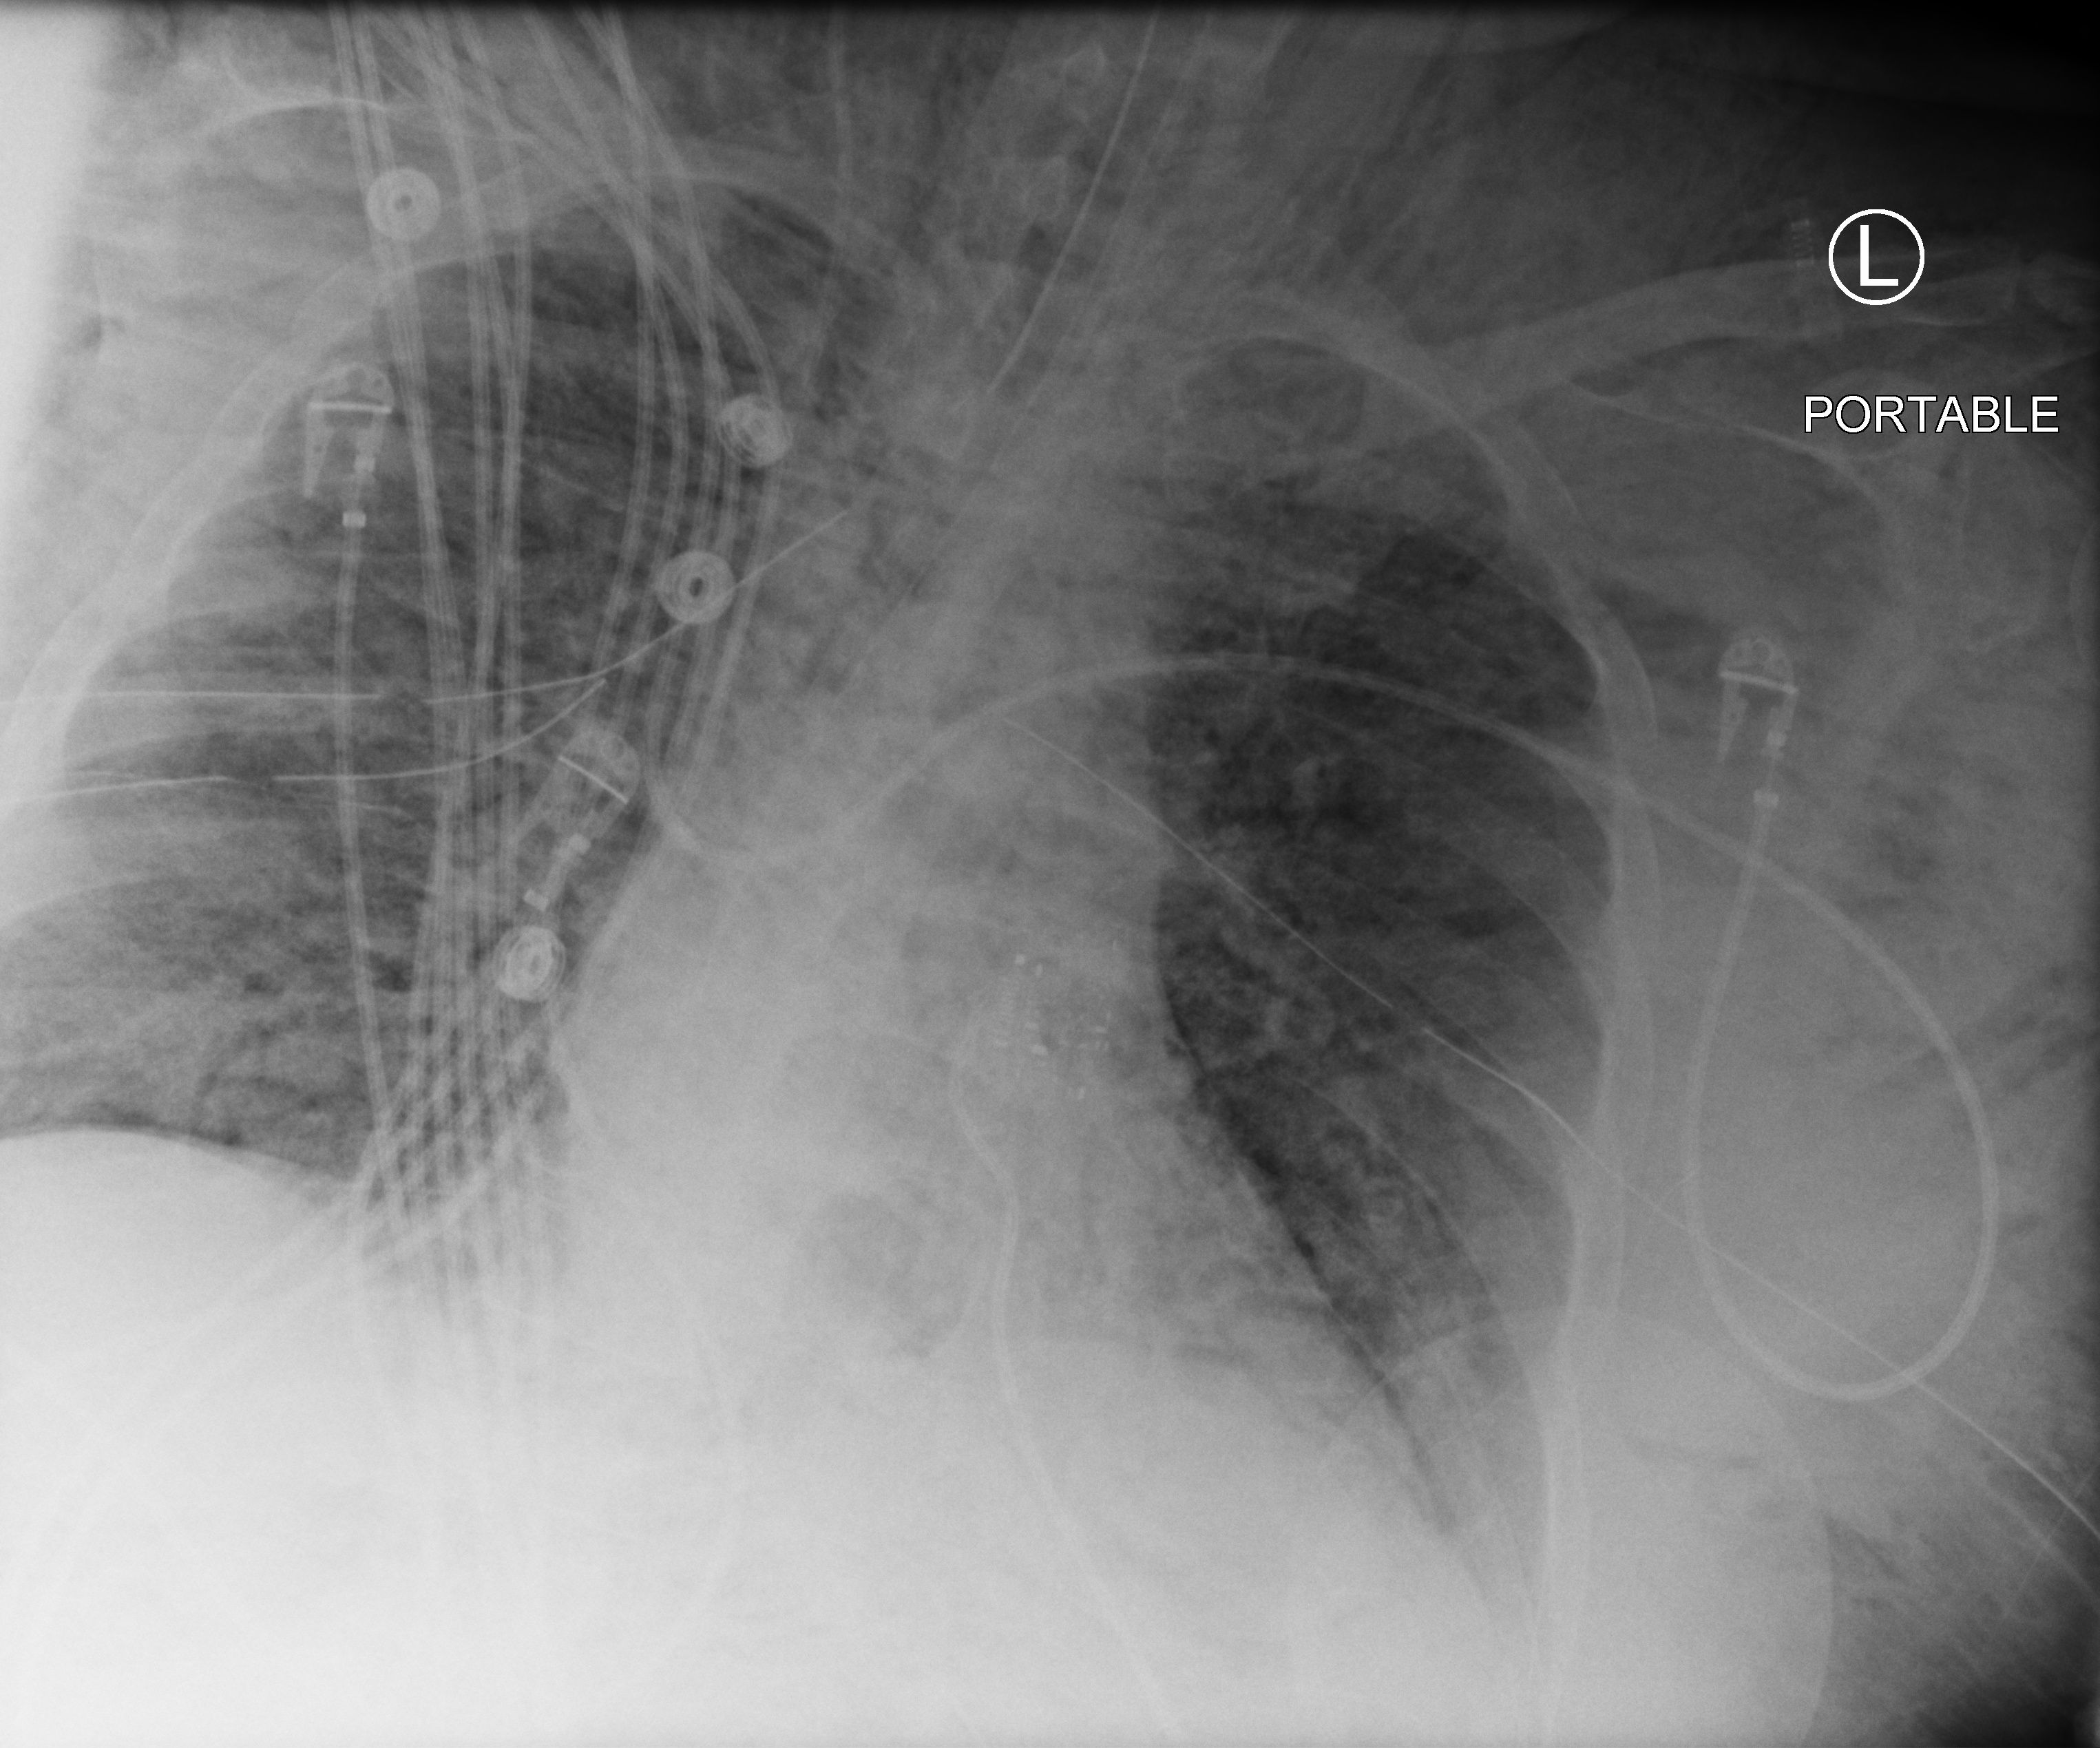
Portable chest radiograph, anteroposterior (AP) projection. Adult patient hospitalised with COVID-19, age 18–59 years.
From the hospital-stay record, not from the radiograph (when in the stay this image was taken is not recorded): admitted to intensive care during this hospital stay: yes; other chronic lung disease (admission record): no; mechanically ventilated during this hospital stay: yes.